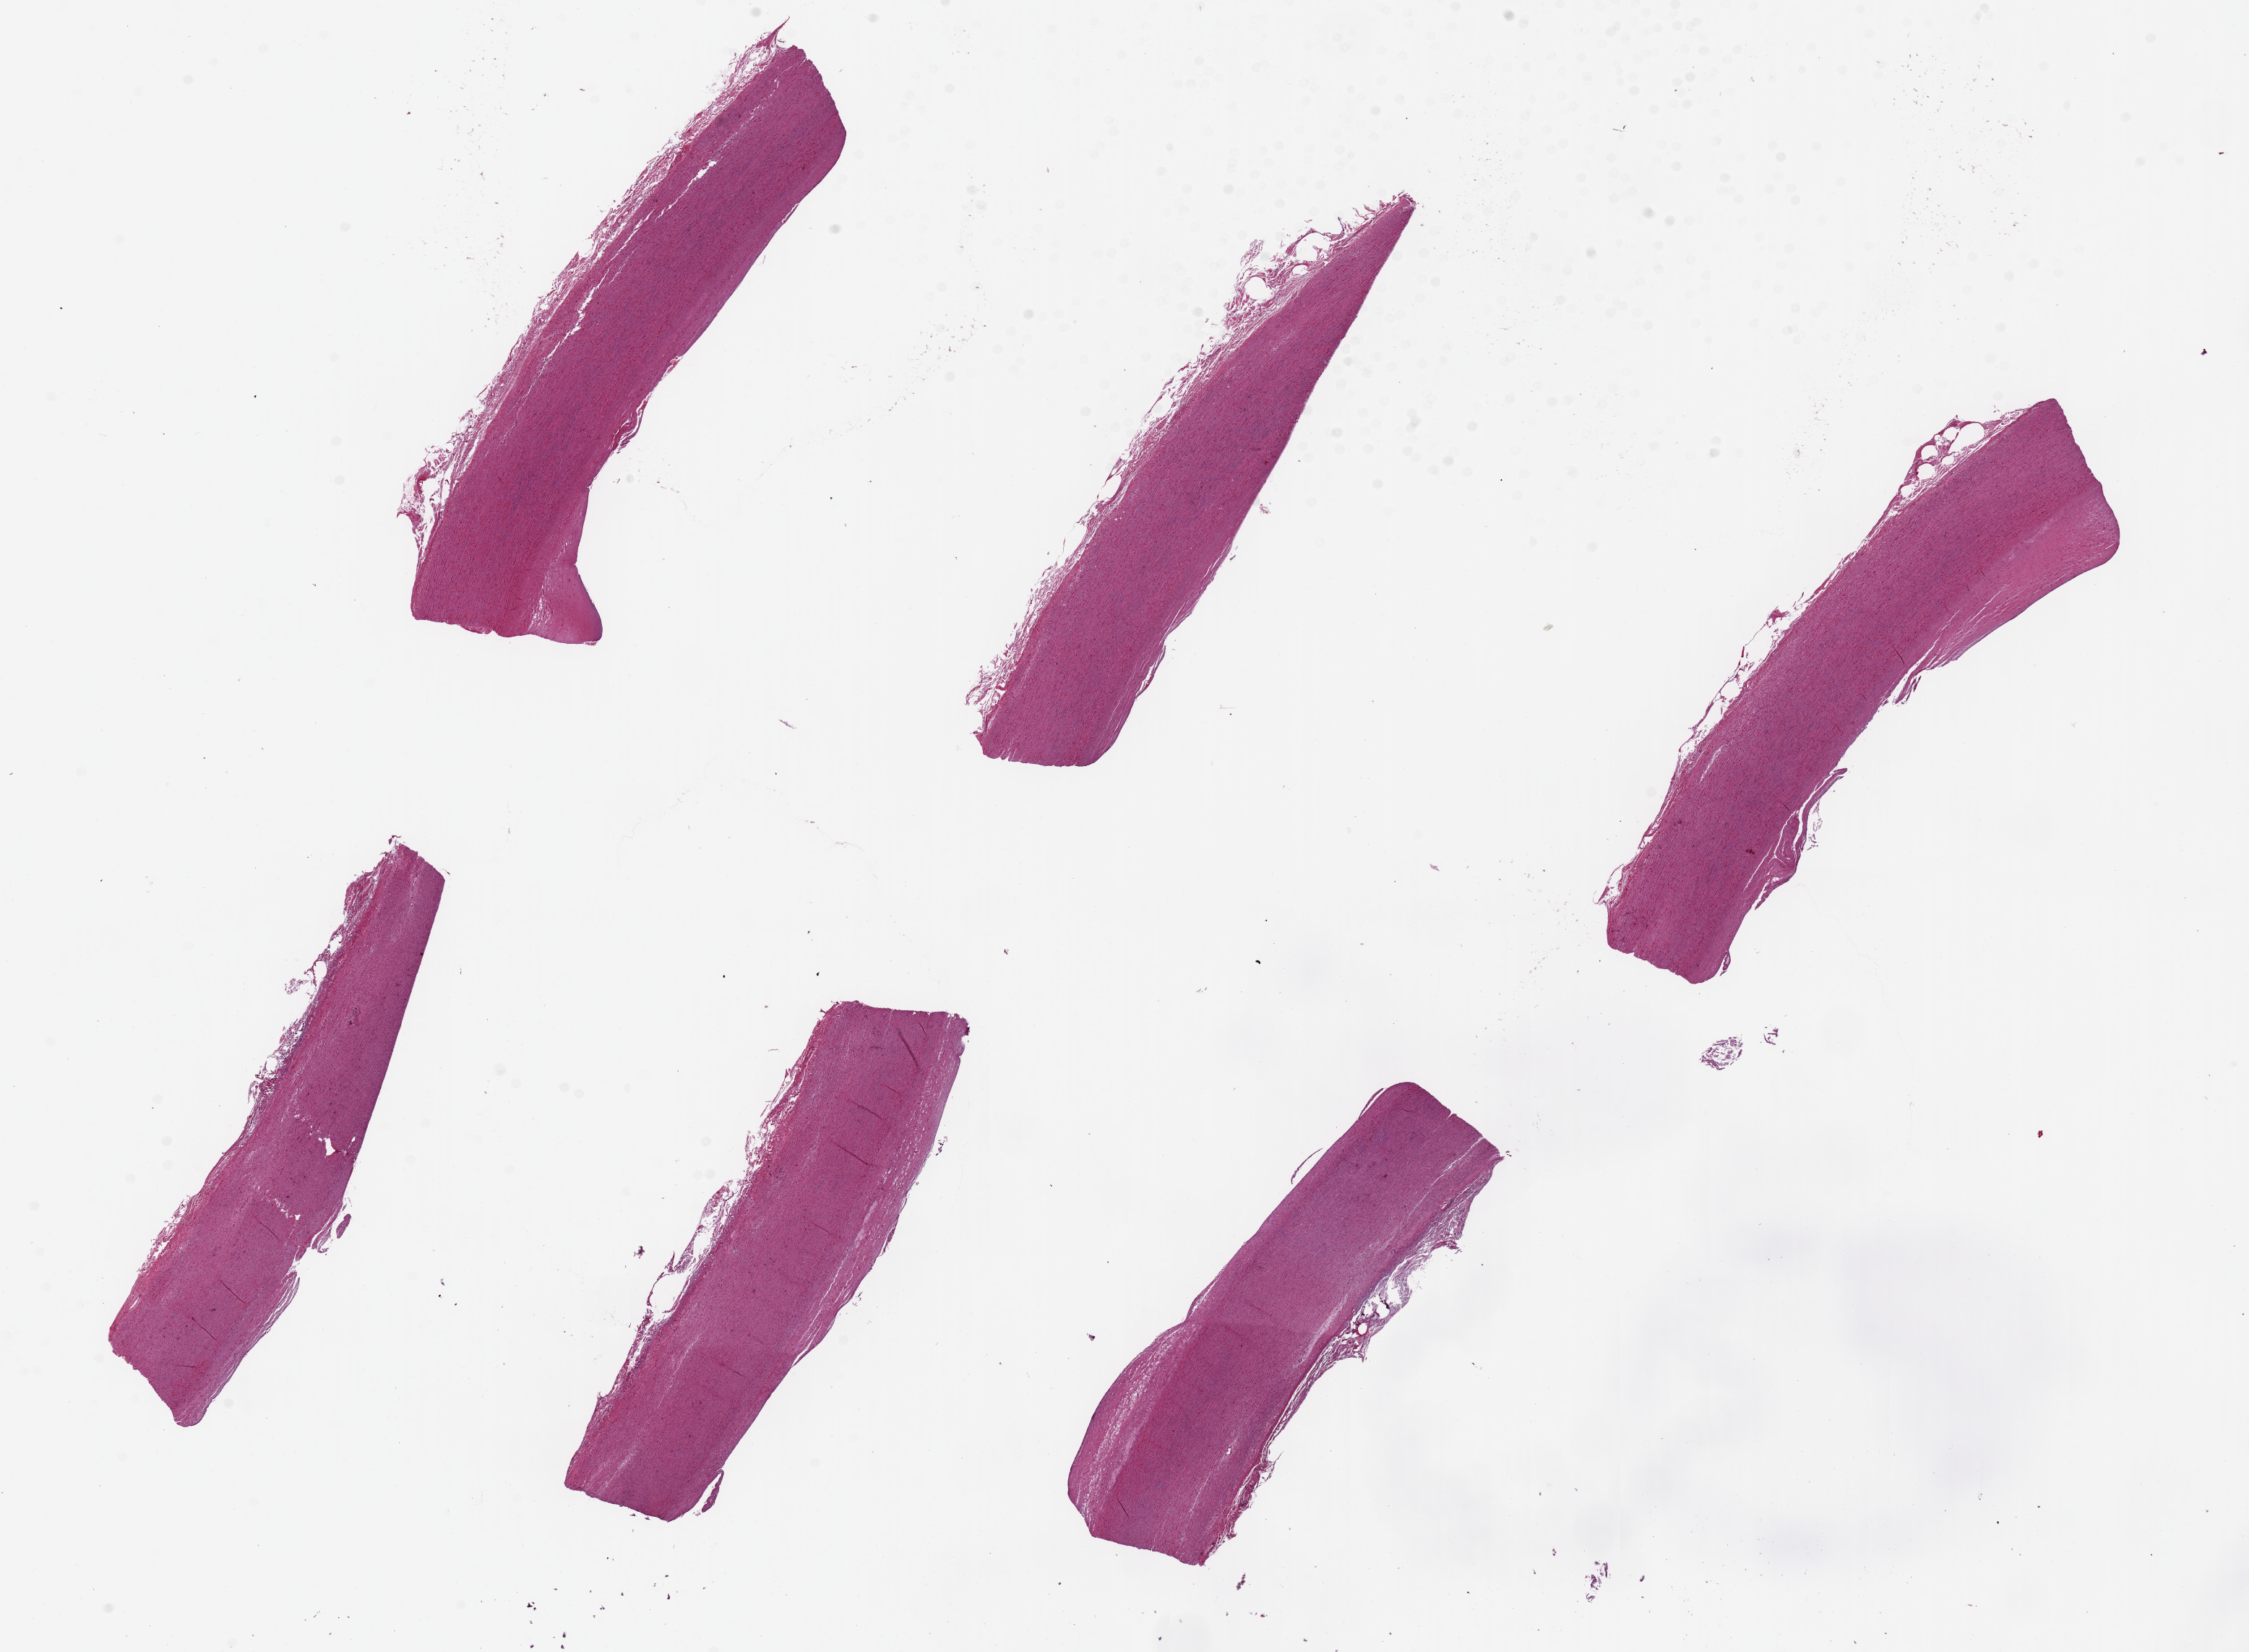
Whole-slide image, hematoxylin and eosin (H&E) stain, whole scanned area (about 24.6 x 18.1 mm, from a 20x scan) shown as a low-resolution overview, PAXgene-fixed paraffin-embedded (PFPE) section, sampled site (target tissue): aorta, tissue donor sample. Female donor.
Reviewer comment on this tissue sample: 6 pieces. up to 8x3mm; well dissected; flat plaques.